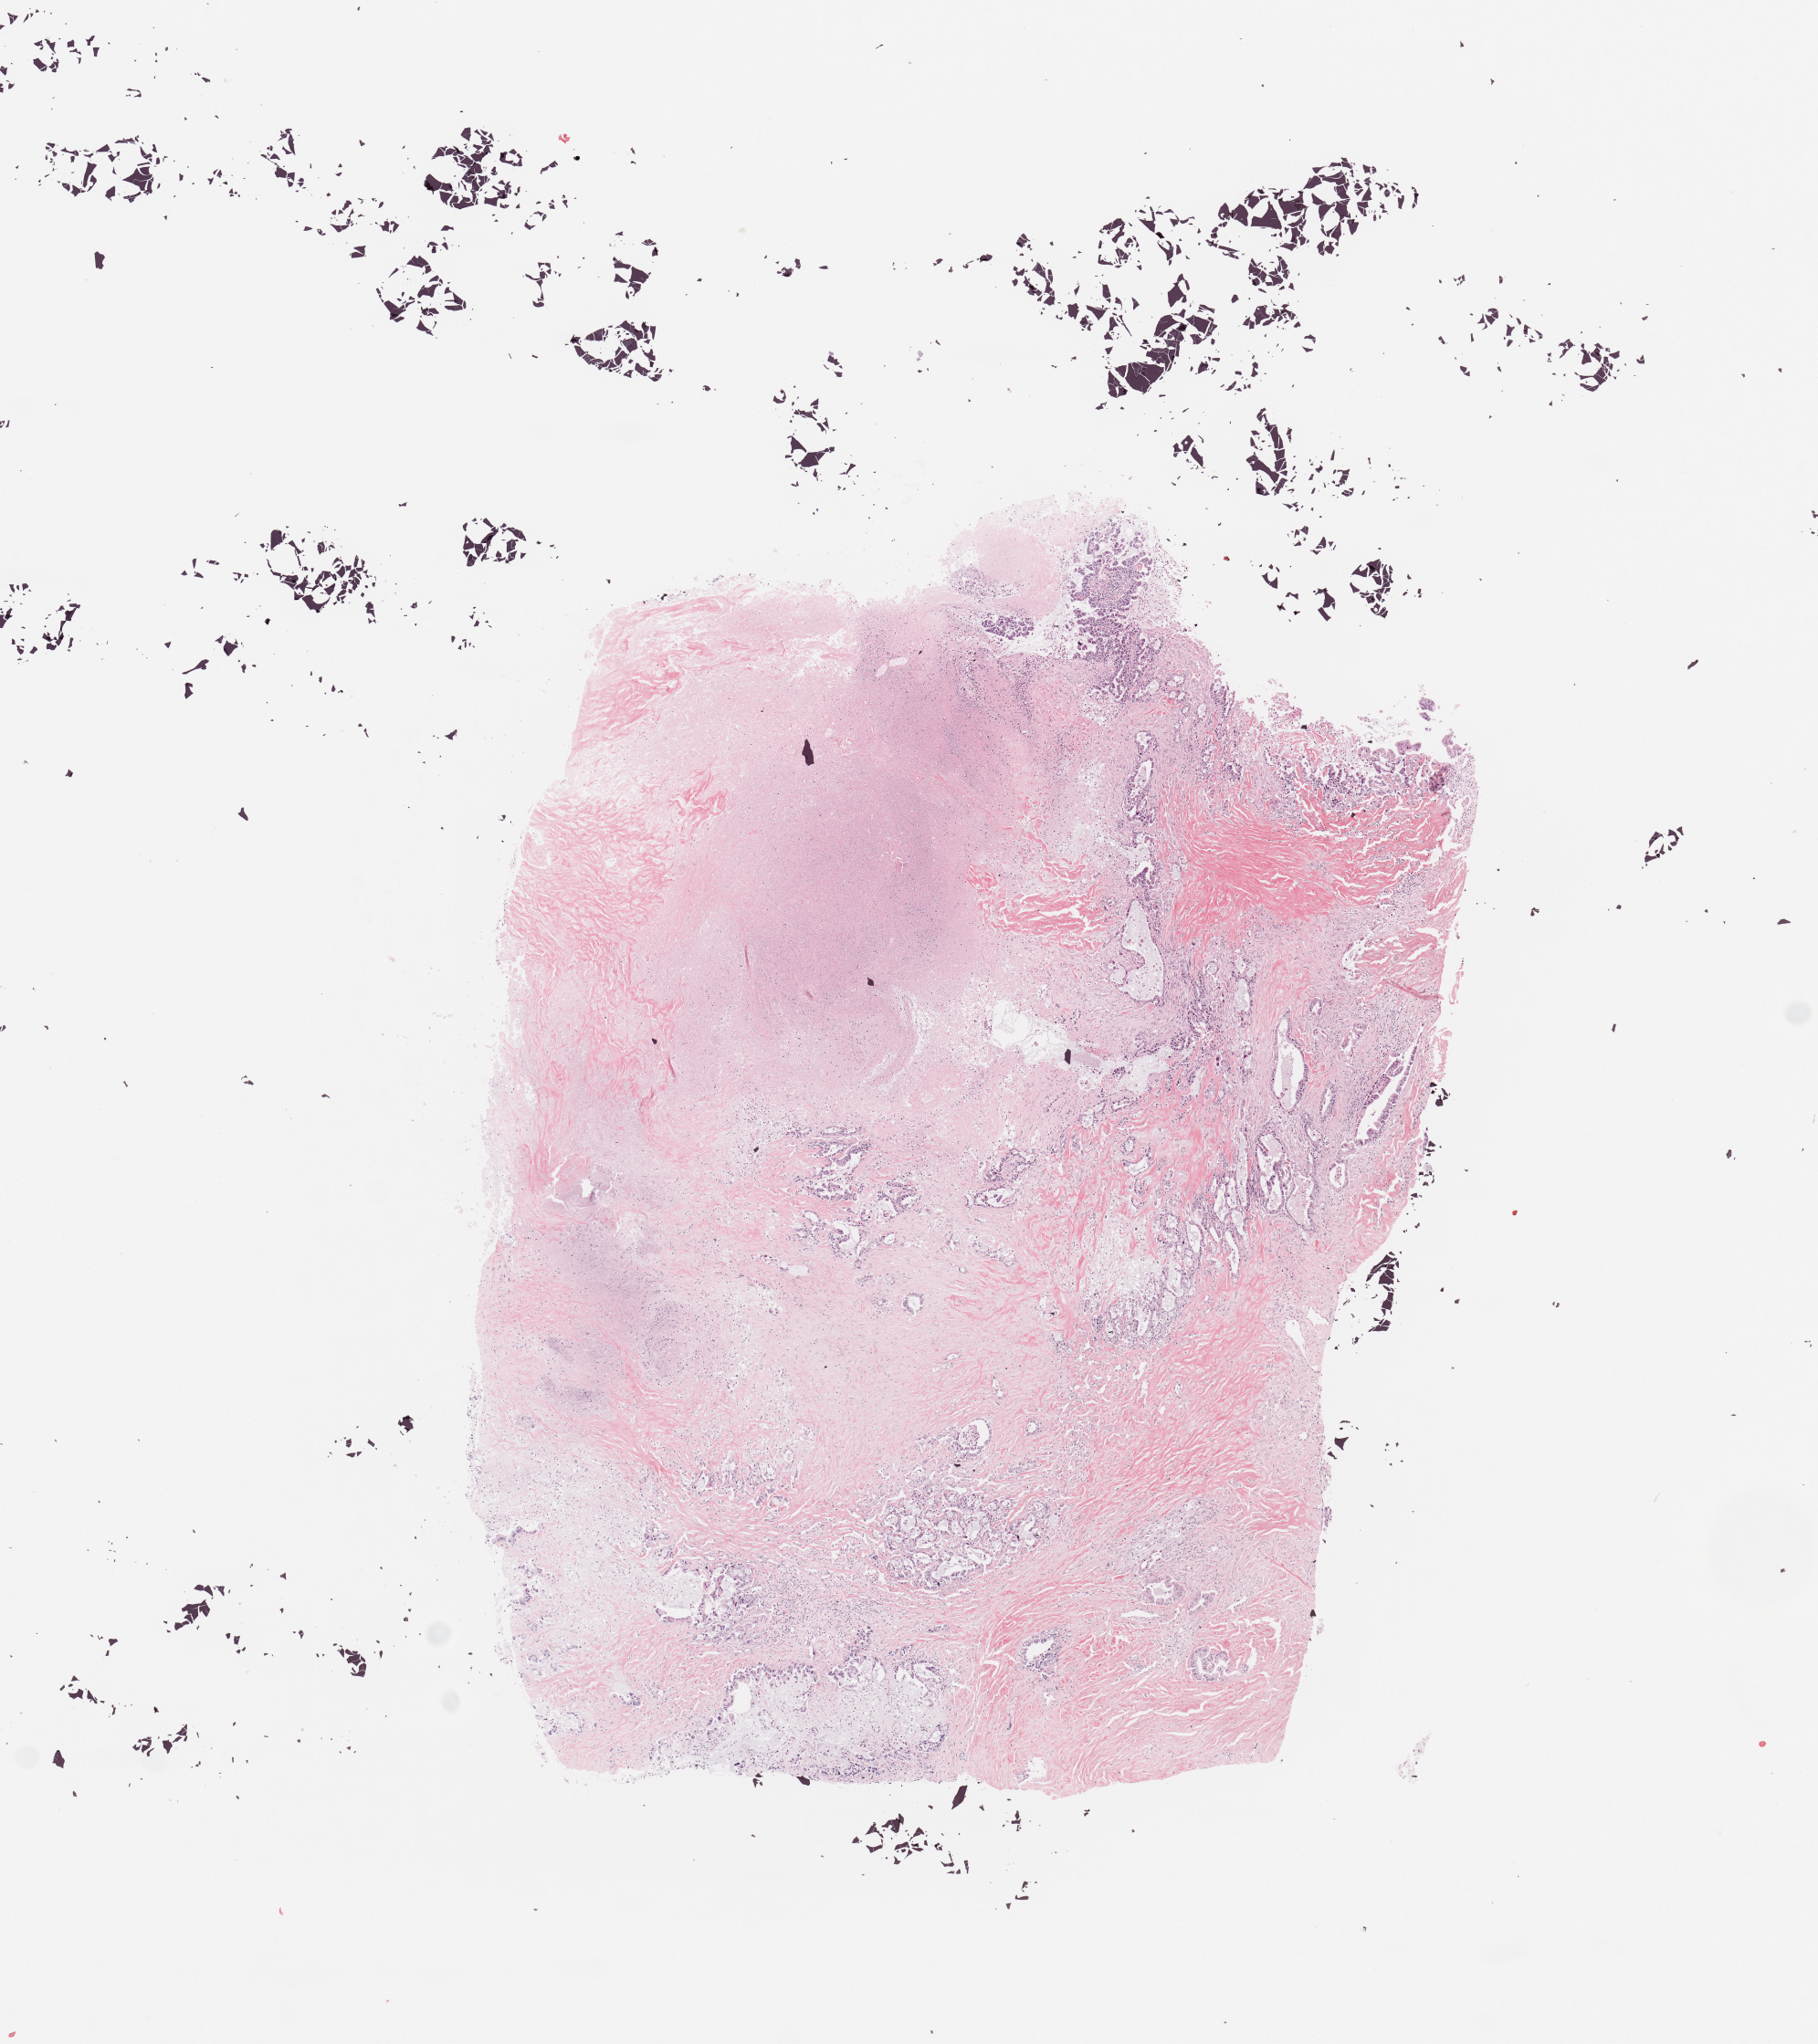
Hematoxylin and eosin (H&E) stained whole-slide image — a low-resolution overview of the entire scanned area, about 7.9 x 8.9 mm (from a 20x scan); pancreas, tumour tissue. 61-year-old female patient. Histologic grade: G2 (moderately differentiated).
* AJCC pathologic stage: IB
* diagnosis: Infiltrating duct carcinoma, NOS